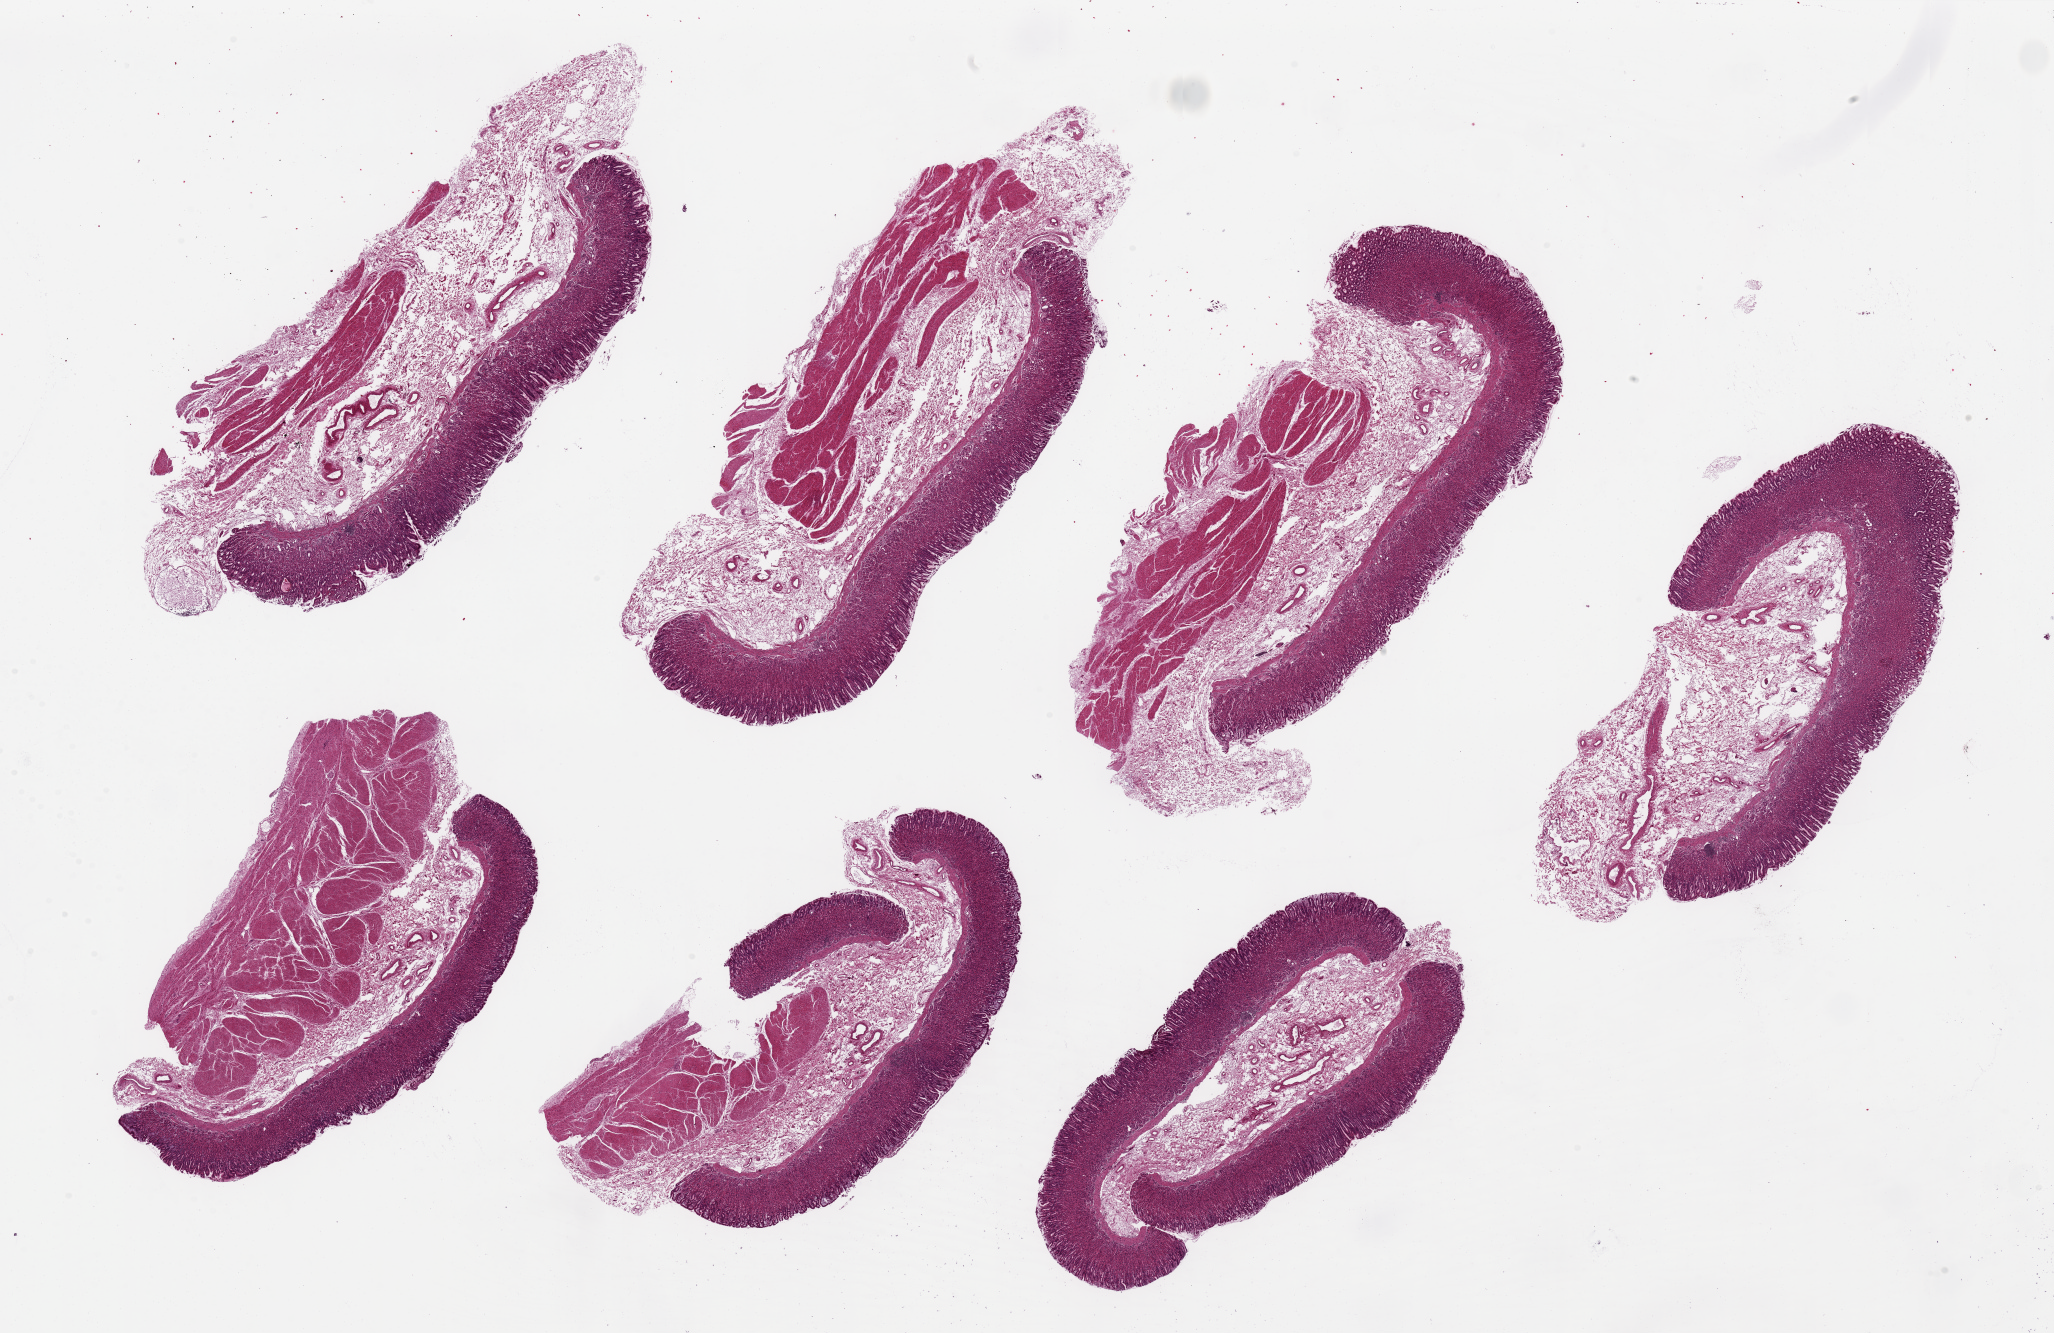
Whole-slide image, hematoxylin and eosin (H&E) stain — low-resolution overview of the scanned area, about 32.5 x 21.1 mm, PAXgene-fixed paraffin-embedded (PFPE) section, target tissue: stomach, tissue donor sample. Donor: female.
Reviewer comment on this tissue sample: 7 pieces up to 10x4 mm; mucosa ~1 mm thick.